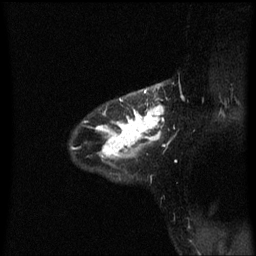
Breast MRI (dynamic contrast-enhanced), one sagittal slice; slice 45 of 60 in the series (ordered by position); dynamic contrast-enhanced series, image 2 of 3 at this slice position (ordered by acquisition); 1.5 T; TE 4.2 ms, TR 8.4 ms; 2 mm slice thickness; 256 × 256 image matrix. Female patient, age 32 years.
Annotated regions visible in this slice (semi-automatic segmentation, software-assisted and operator-edited):
- analysis volume of interest (the breast-tissue region the enhancement analysis was run in; not a lesion): box from (x=77, y=84) to (x=165, y=167) px
- tumour enhancement mask (voxels above the 70 % enhancement threshold inside the analysis volume of interest): (x=97, y=84)–(x=165, y=159)